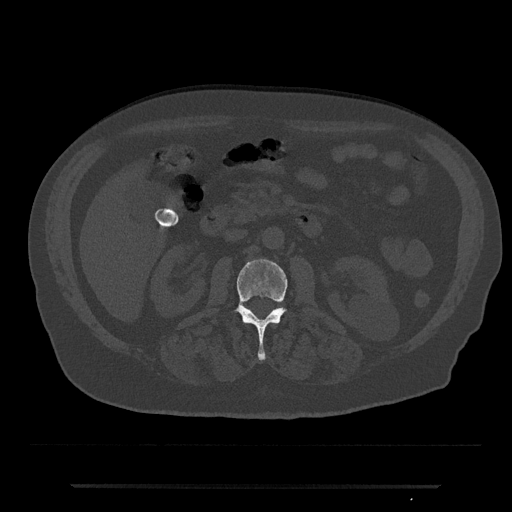
CT including the spine, one axial slice; position 469 of 797 along the scan axis; bone window (W 1800 / L 400 HU); 512 × 512 image matrix, field of view 434 × 434 mm. Patient: male, 80 years. From the clinical record (not read from this slice): primary cancer: prostate.
Annotated regions visible in this slice (semi-automatically segmented with operator editing):
- L2 vertebra: bounding box (x1, y1, x2, y2) in pixels: (236, 259, 288, 361)